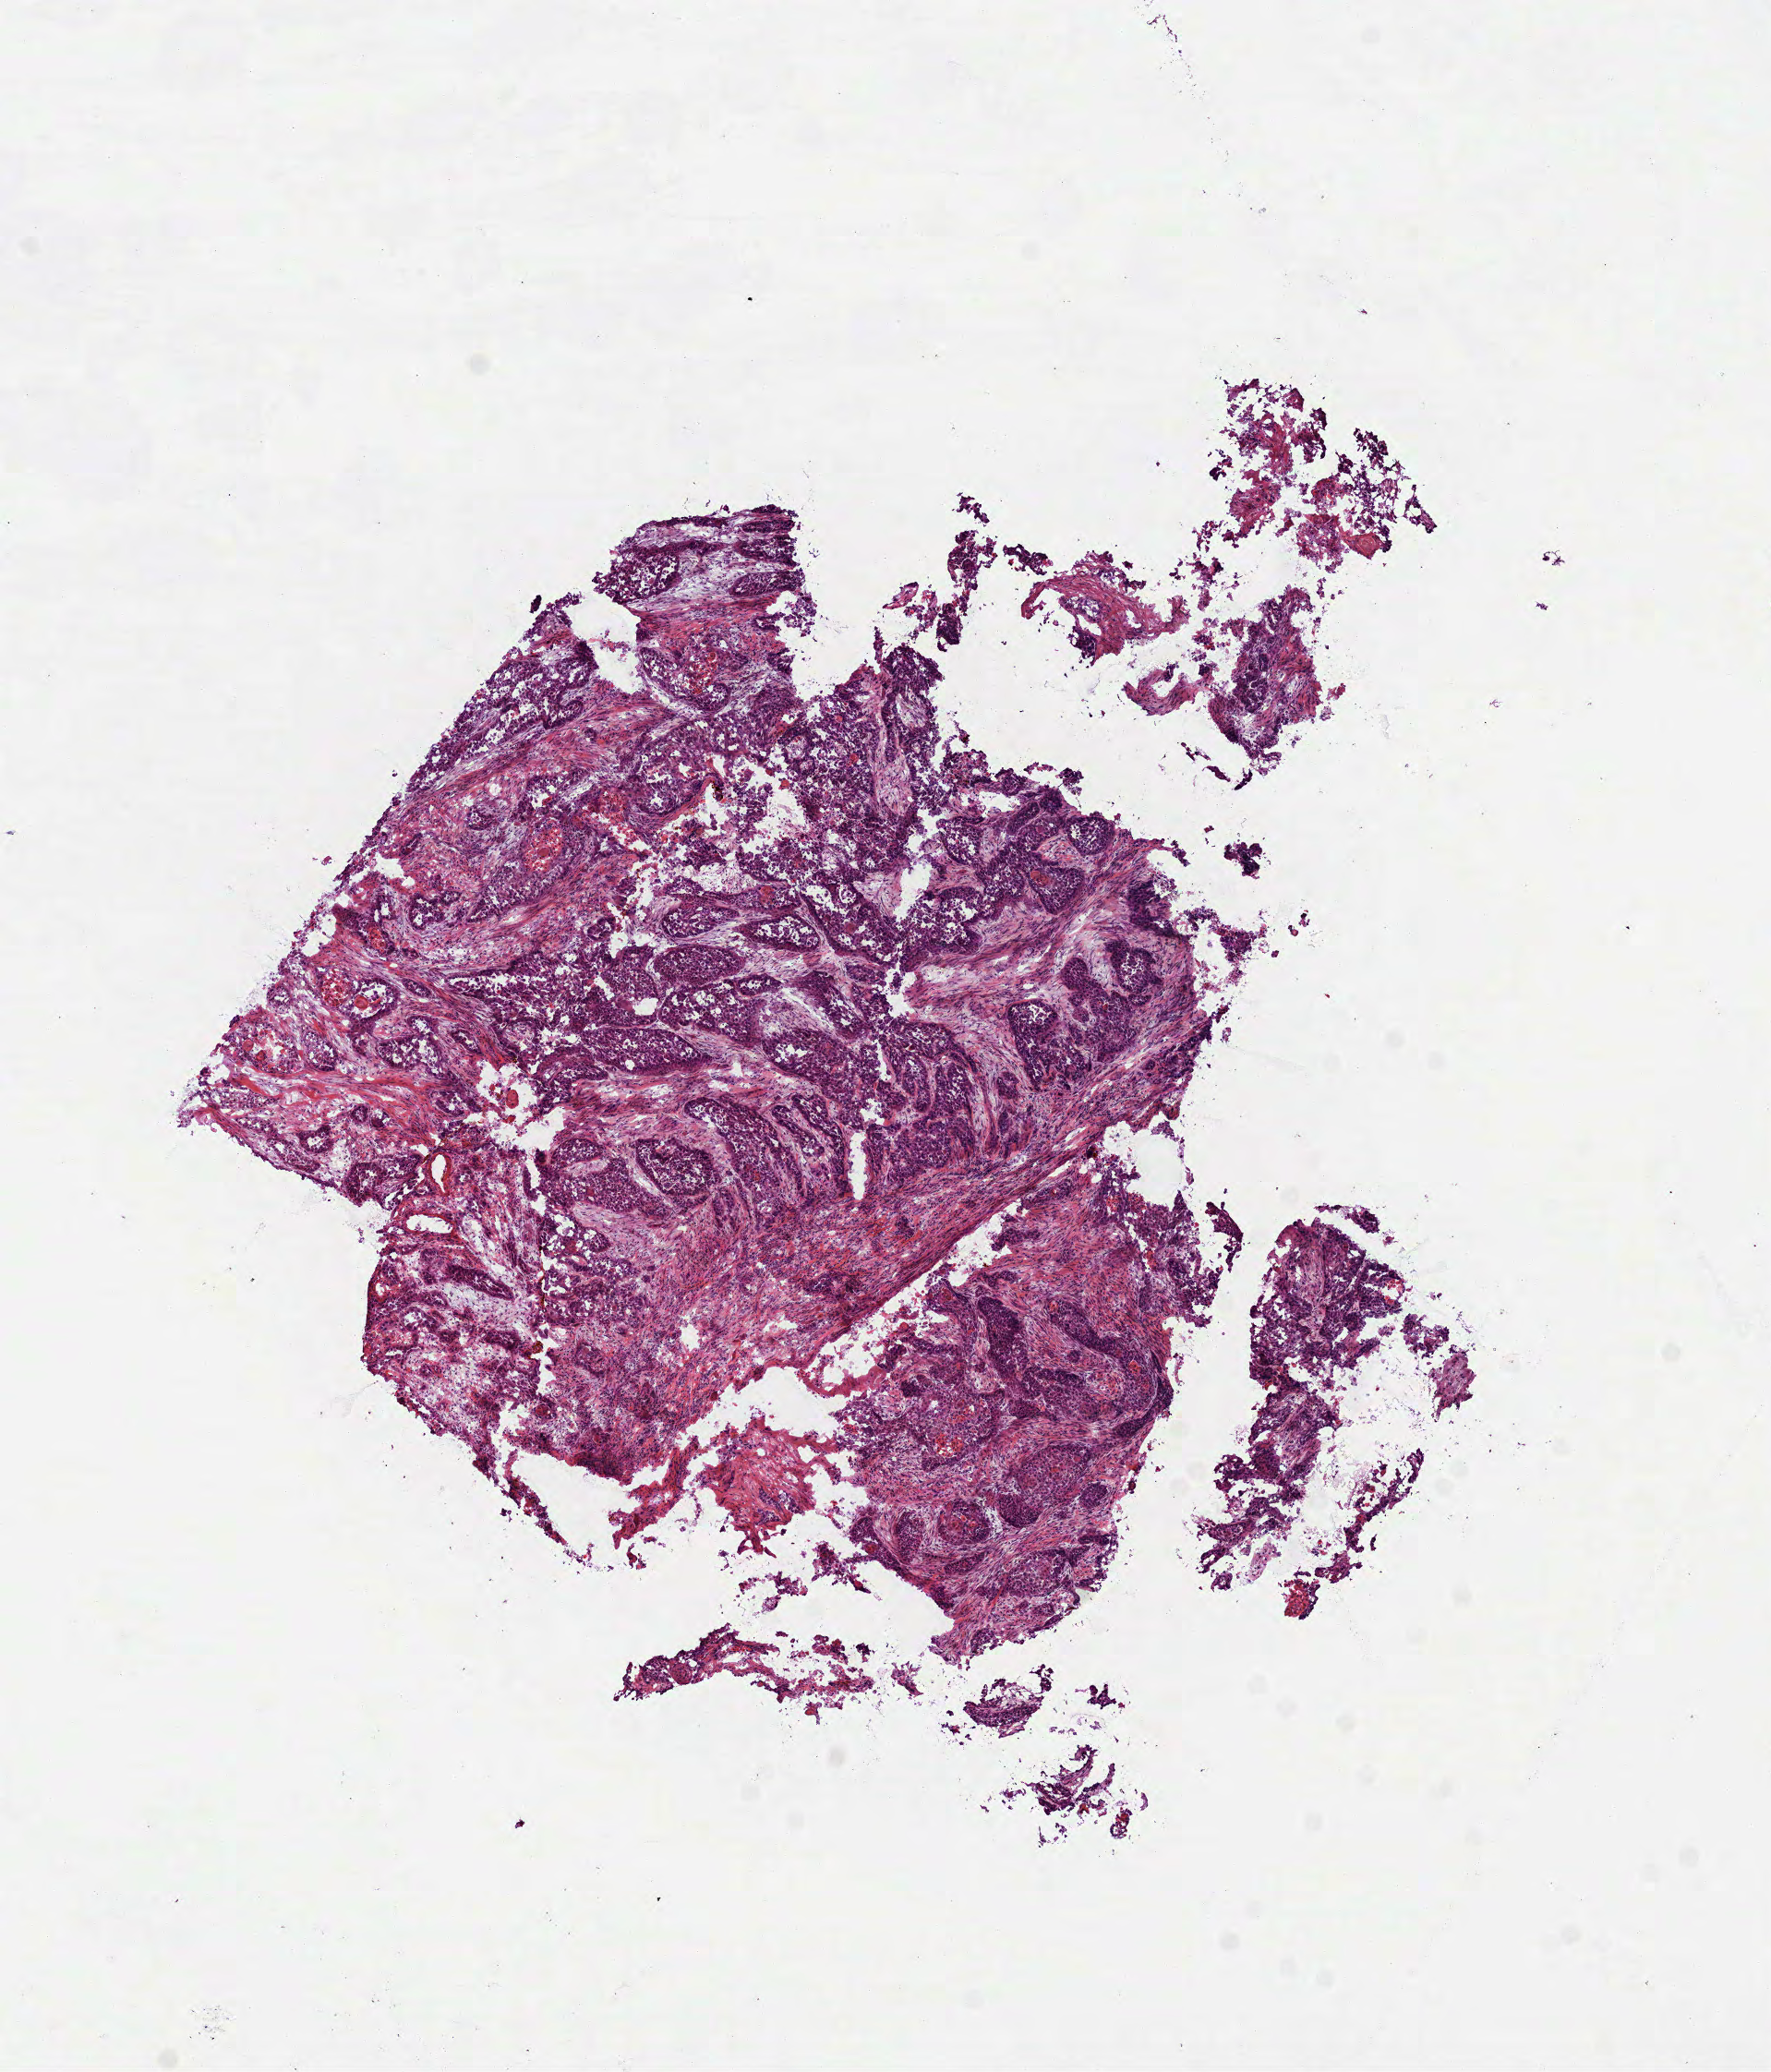
Whole-slide histology image, H&E-stained, whole scanned area (about 7.7 x 9.0 mm, slide scanned at 40x) shown as a low-resolution overview, frozen section from the bottom of the tissue portion, primary tumour sample from the head and neck. Female patient; age at initial diagnosis 80 years. Pathologist review of this section (percent, as recorded): tumour cells 98%, tumour nuclei 75%.
Diagnosis: Squamous cell carcinoma, NOS (cheek mucosa).